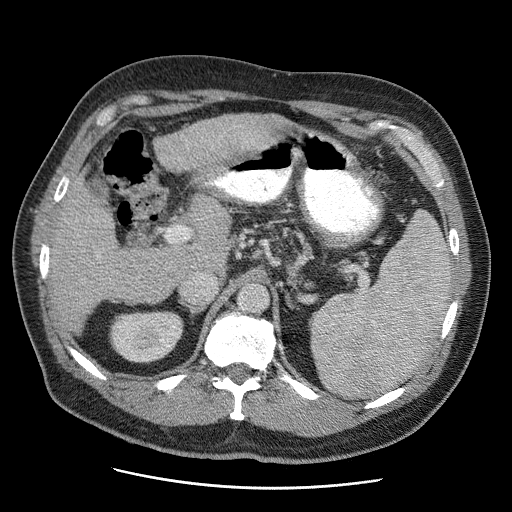
Contrast-enhanced abdominal CT (liver protocol), one axial slice; slice 26 of 81 in the series (ordered by position); 120 kVp; soft-tissue window (W 400 / L 40 HU); 512 × 512 image matrix, field of view 380 × 380 mm. Case-level facts recorded for this patient, not image findings: diagnosis: hepatocellular carcinoma (patient treated with transarterial chemoembolisation; whether this scan precedes or follows treatment is not stated here); TNM stage (as recorded): Stage-IIIA; Child-Pugh class: A; tumour nodularity: multinodular.
Structures marked on this image (semi-automatic segmentation, software-assisted and operator-edited):
- abdominal aorta: bounding box (x1, y1, x2, y2) in pixels: (240, 285, 268, 313)
- liver parenchyma outside the tumour (the mass and vessels are separate outlines, so this box may not span the whole liver): (50, 114, 290, 332)